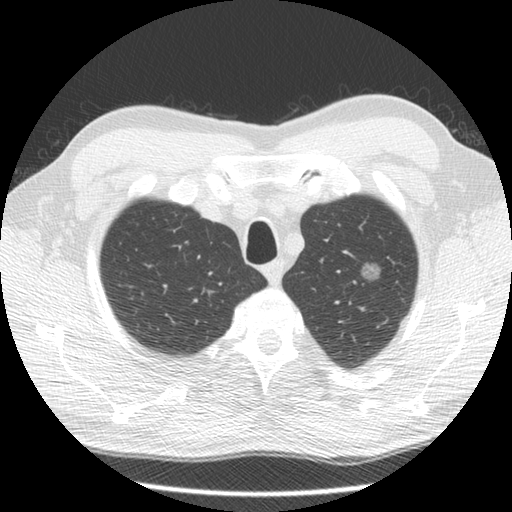
Low-dose screening chest CT, one axial slice; slice 115 of 132 in the series (ordered by position); lung window (W 1500 / L -600 HU); 512 × 512 image matrix, field of view 340 × 340 mm.
Annotated regions visible in this slice (expert manual segmentation):
- lesion 1 (tumor, upper lobe of left lung): bounding box [x1, y1, x2, y2] px = [355, 263, 380, 283]